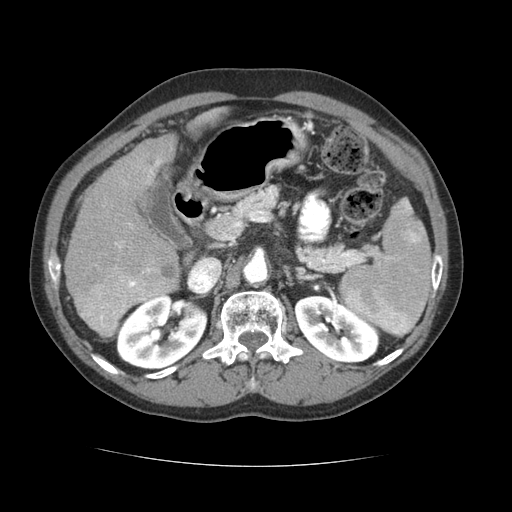
Contrast-enhanced abdominal CT (liver protocol), one axial slice; slice 37 of 69 in the series (ordered by position); reconstruction kernel STANDARD; 120 kVp; soft-tissue window (W 400 / L 40 HU); 2.5 mm slice thickness; 512 × 512 image matrix. From the clinical record (not read from this slice): diagnosis: hepatocellular carcinoma (patient treated with transarterial chemoembolisation; whether this scan precedes or follows treatment is not stated here); TNM stage (as recorded): Stage-II; Child-Pugh class: B; tumour differentiation: poorly differentiated; tumour size: 2.6 cm.
Annotated regions visible in this slice (semi-automatically segmented with operator editing):
- liver parenchyma outside the tumour (the mass and vessels are separate outlines, so this box may not span the whole liver): bounding box [x1, y1, x2, y2] px = [64, 108, 226, 335]
- mass: [73, 254, 179, 337]
- liver vessels: [115, 160, 160, 248]